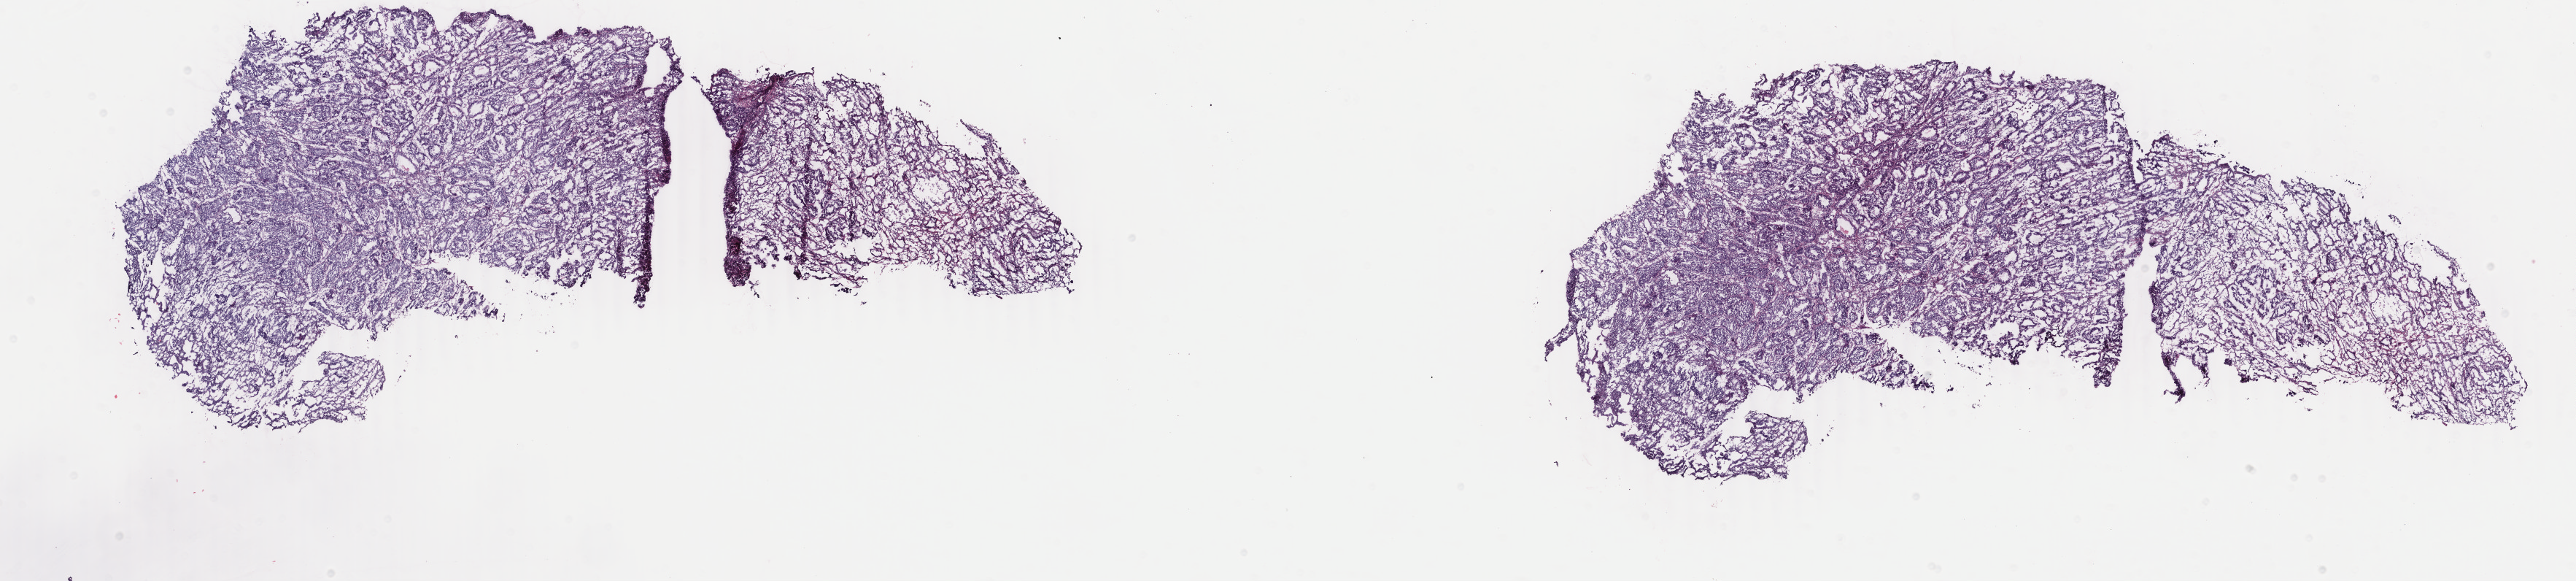
Whole-slide histology image, Hematoxylin and eosin (H&E) stained, a low-resolution overview of the entire scanned area, about 28.1 x 6.3 mm (slide scanned at 40x); frozen section from the bottom of the tissue portion; primary tumour sample from the uterus. Female, age 45 years at initial diagnosis. Histologic grade: G2 (moderately differentiated). Slide review estimates, as recorded: tumour cells 100%, tumour nuclei 80%, normal cells 0%, stromal cells 0%, necrosis 0%. Inflammatory infiltration, as recorded: lymphocyte infiltration 0%, monocyte infiltration 0%, neutrophil infiltration 0%.
FIGO stage: IA. Histologic diagnosis: Endometrioid adenocarcinoma, NOS (endometrium).